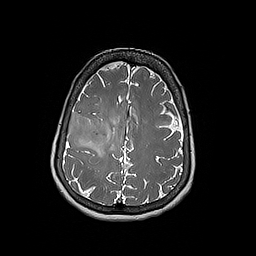
Brain MRI from a brain-tumour surgery series, one axial slice. Slice 67 of 192 in the series (ordered by position). 1 mm slice thickness. 256 × 256 image matrix, field of view 250 × 250 mm. From the clinical record (not read from this slice): histopathology: Oligodendroglioma; WHO grade: 3; IDH mutation: yes; tumour location: Right Frontal.
Outlined on this slice (manually delineated by an expert):
- tumour: bounding box [x1, y1, x2, y2] px = [67, 111, 108, 148]